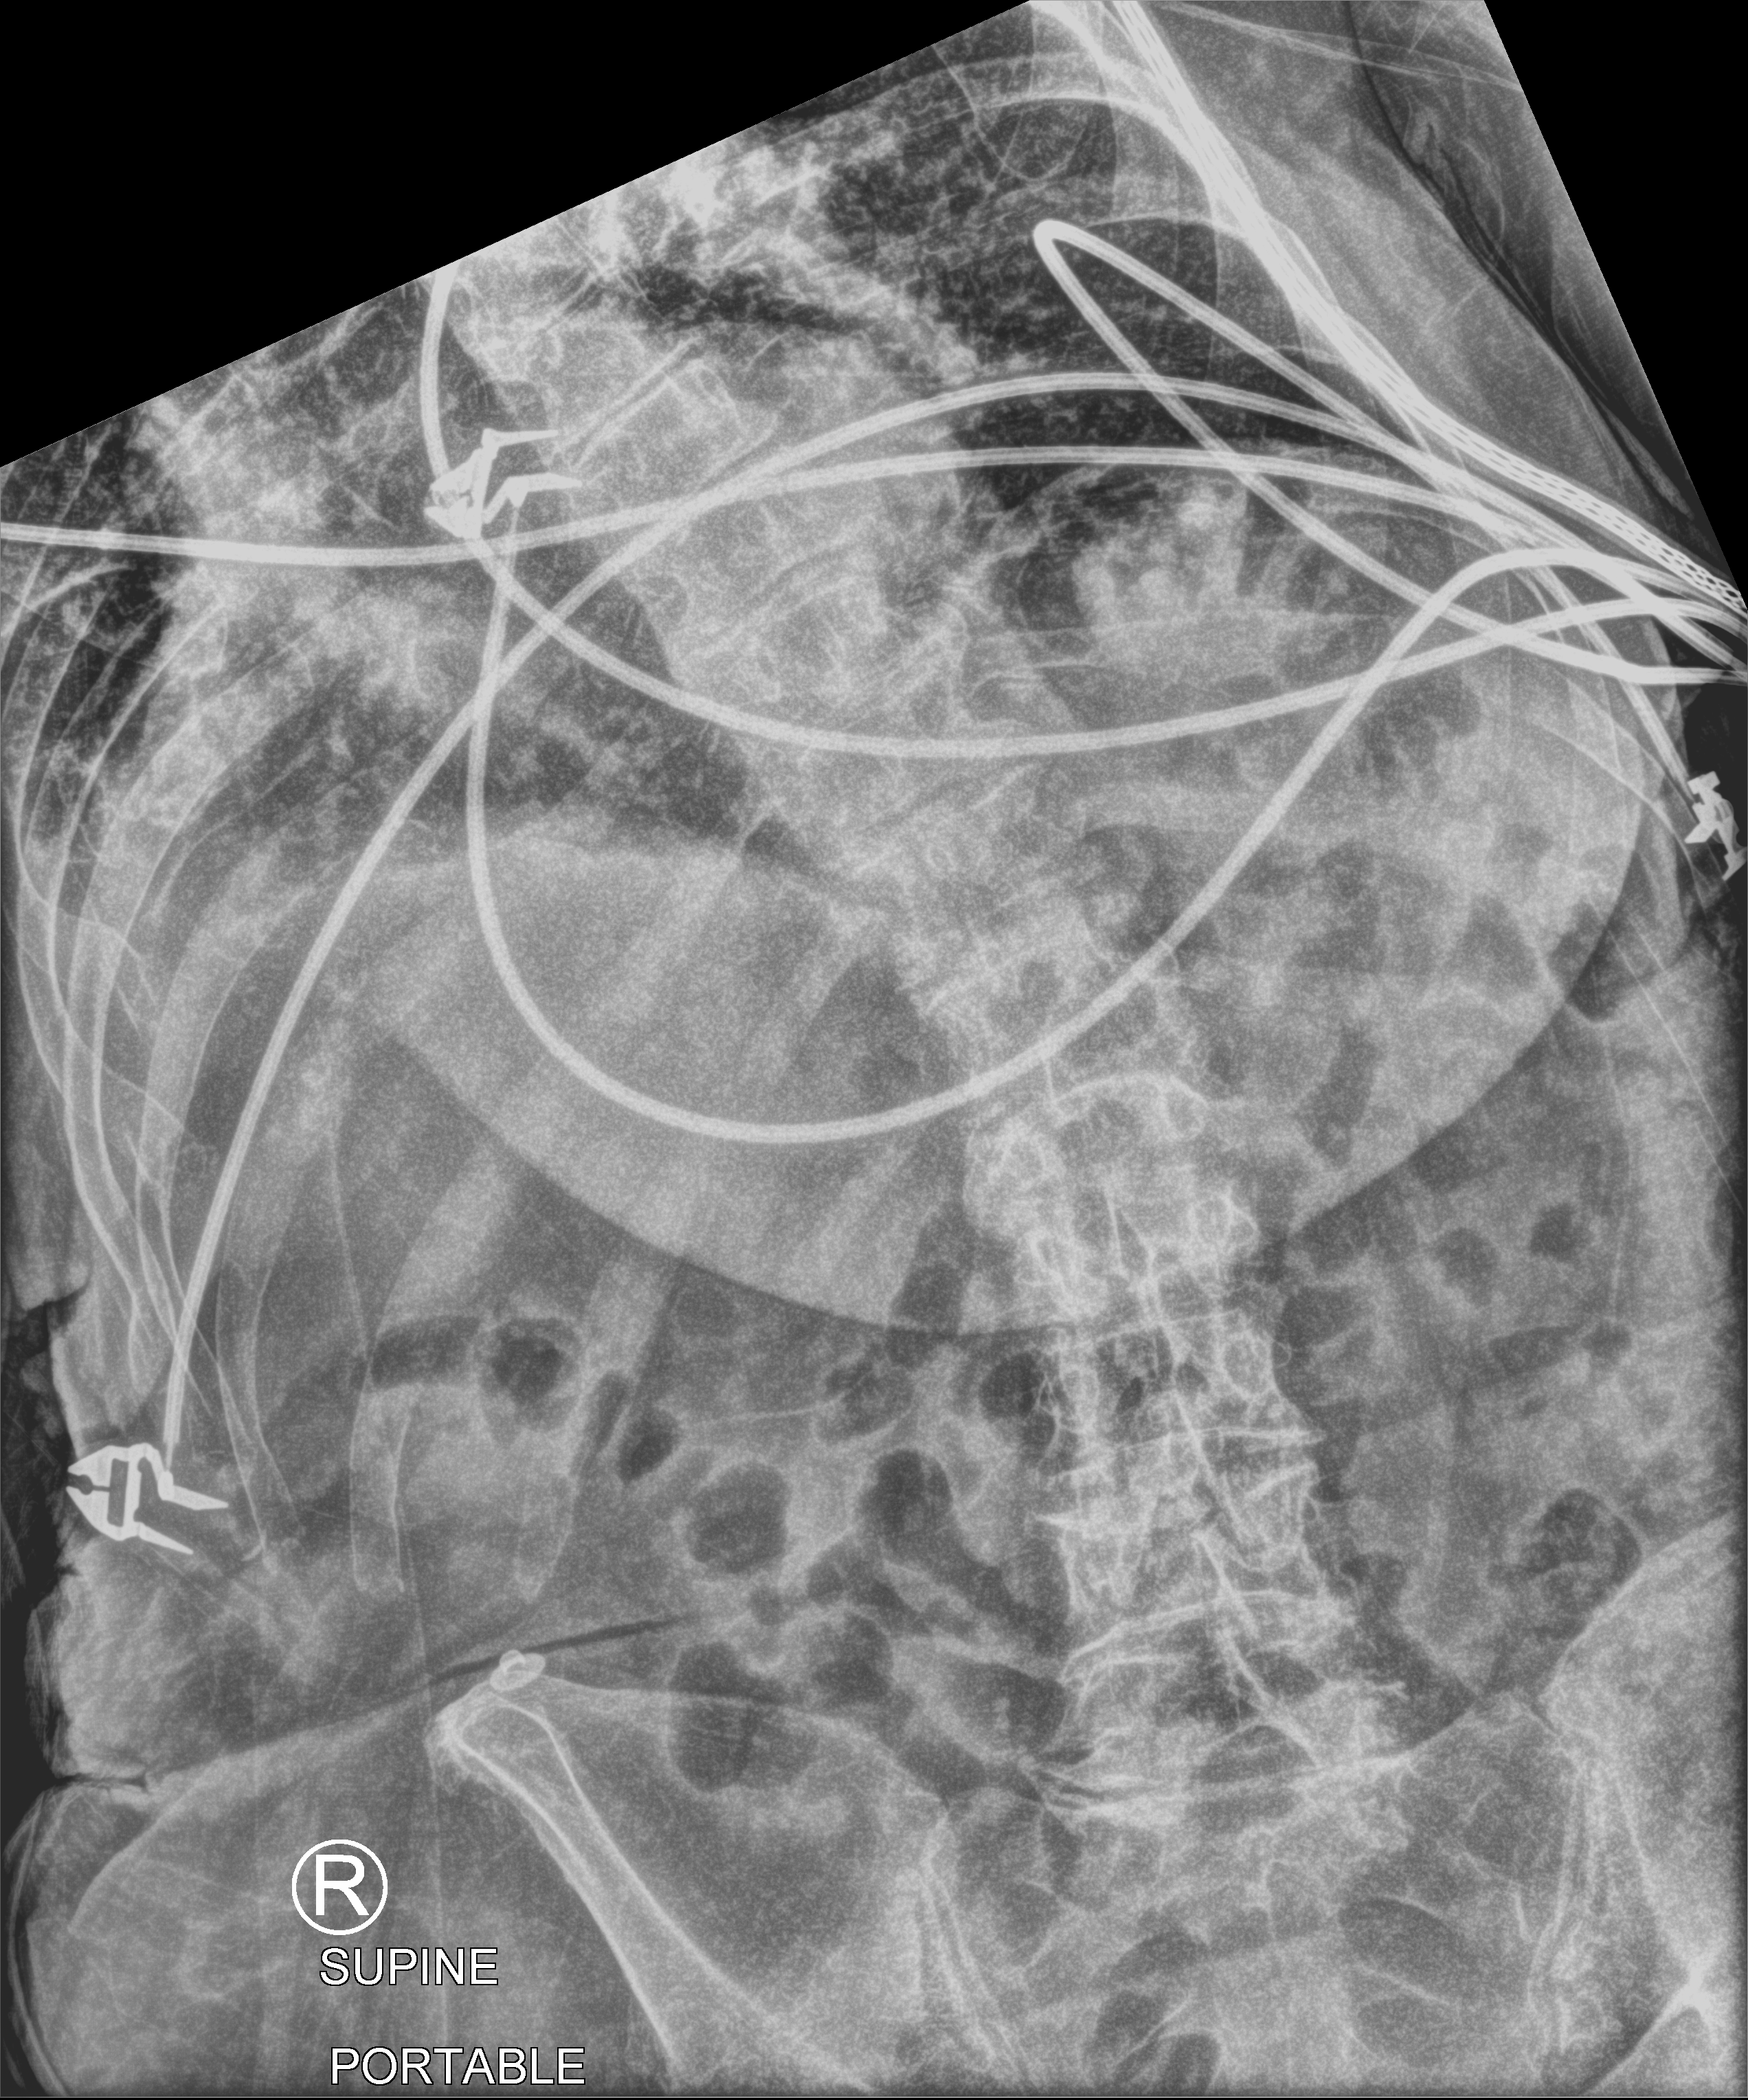
Portable abdomen radiograph; anteroposterior (AP) projection. Patient hospitalised with COVID-19; female, aged 75–90 years.
Hospital-stay facts (about this admission, not read from this image; timing relative to this image not recorded): smoking status (admission record): never; mechanically ventilated during this hospital stay: no.